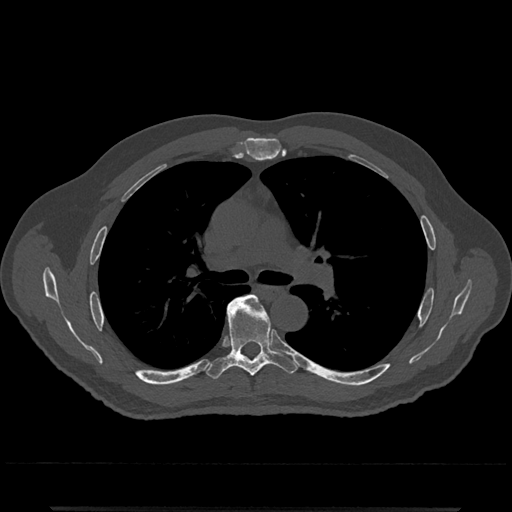
CT including the spine, one axial slice; position 782 of 797 along the scan axis; 120 kVp; bone window (W 1800 / L 400 HU); 0.5 mm slice thickness; 512 × 512 image matrix, field of view 393 × 393 mm. Male patient, age 67 years. Case-level facts recorded for this patient, not image findings: primary cancer: prostate.
Annotated regions visible in this slice (semi-automatic segmentation, software-assisted and operator-edited):
- T5 vertebra: bounding box <243,295,263,309> (left, top, right, bottom; pixels)
- T6 vertebra: <206,295,298,379>